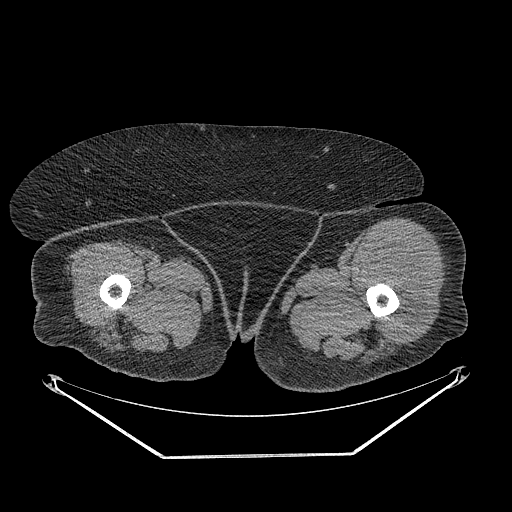
CT of an extremity soft-tissue mass (from a PET/CT study), one axial slice; position 250 of 267 along the scan axis; reconstruction kernel STANDARD; 140 kVp; soft-tissue window (W 400 / L 40 HU); 3.75 mm slice thickness; 512 × 512 image matrix, field of view 500 × 500 mm. Female patient. Case-level facts recorded for this patient, not image findings: histological type: undifferentiated – high grade; grade: high; site of the primary tumour: left thigh.
Structures marked on this image (expert contour drawn on MRI and transferred to this co-registered scan by the dataset authors):
- gross tumour volume including surrounding oedema: bounding box [x1, y1, x2, y2] px = [365, 242, 428, 343]
- gross tumour volume (mass): [367, 244, 428, 341]